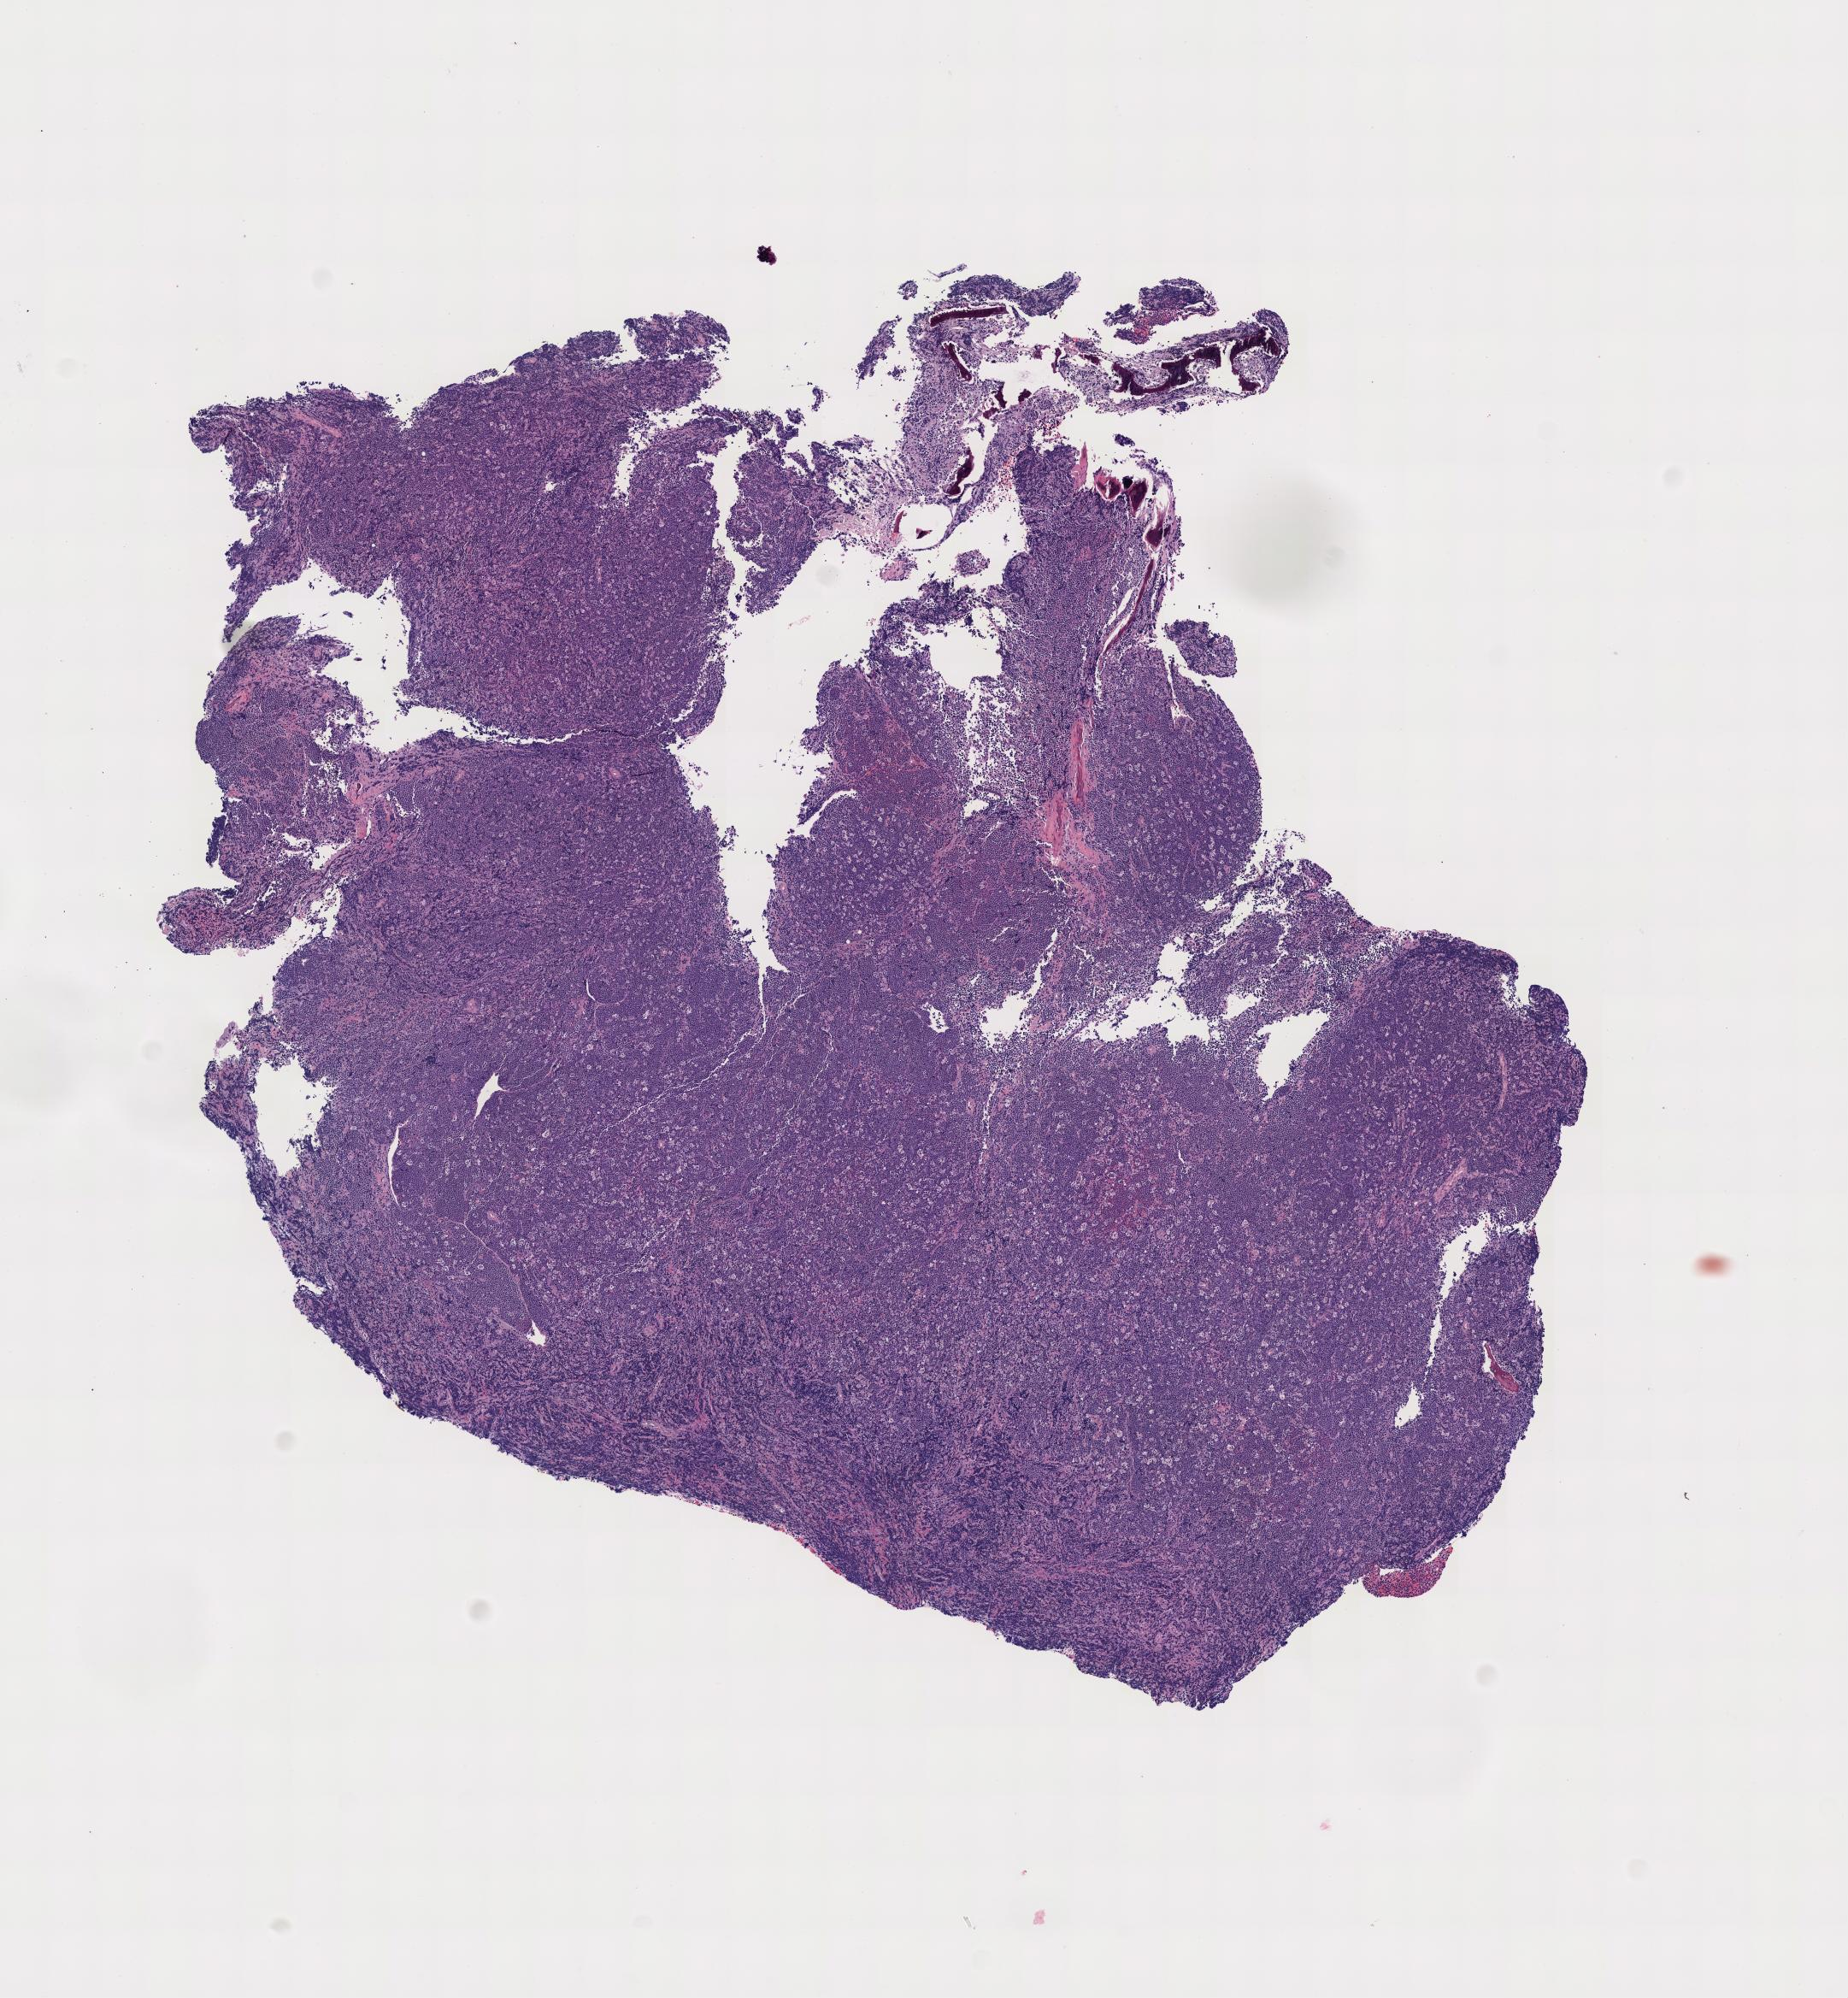
Digitized H&E-stained section — whole scanned area shown as a low-resolution overview. Tumor tissue. Site: cranium. Patient: female, age at initial diagnosis 8 years.
Histologic diagnosis: Burkitt lymphoma, NOS.